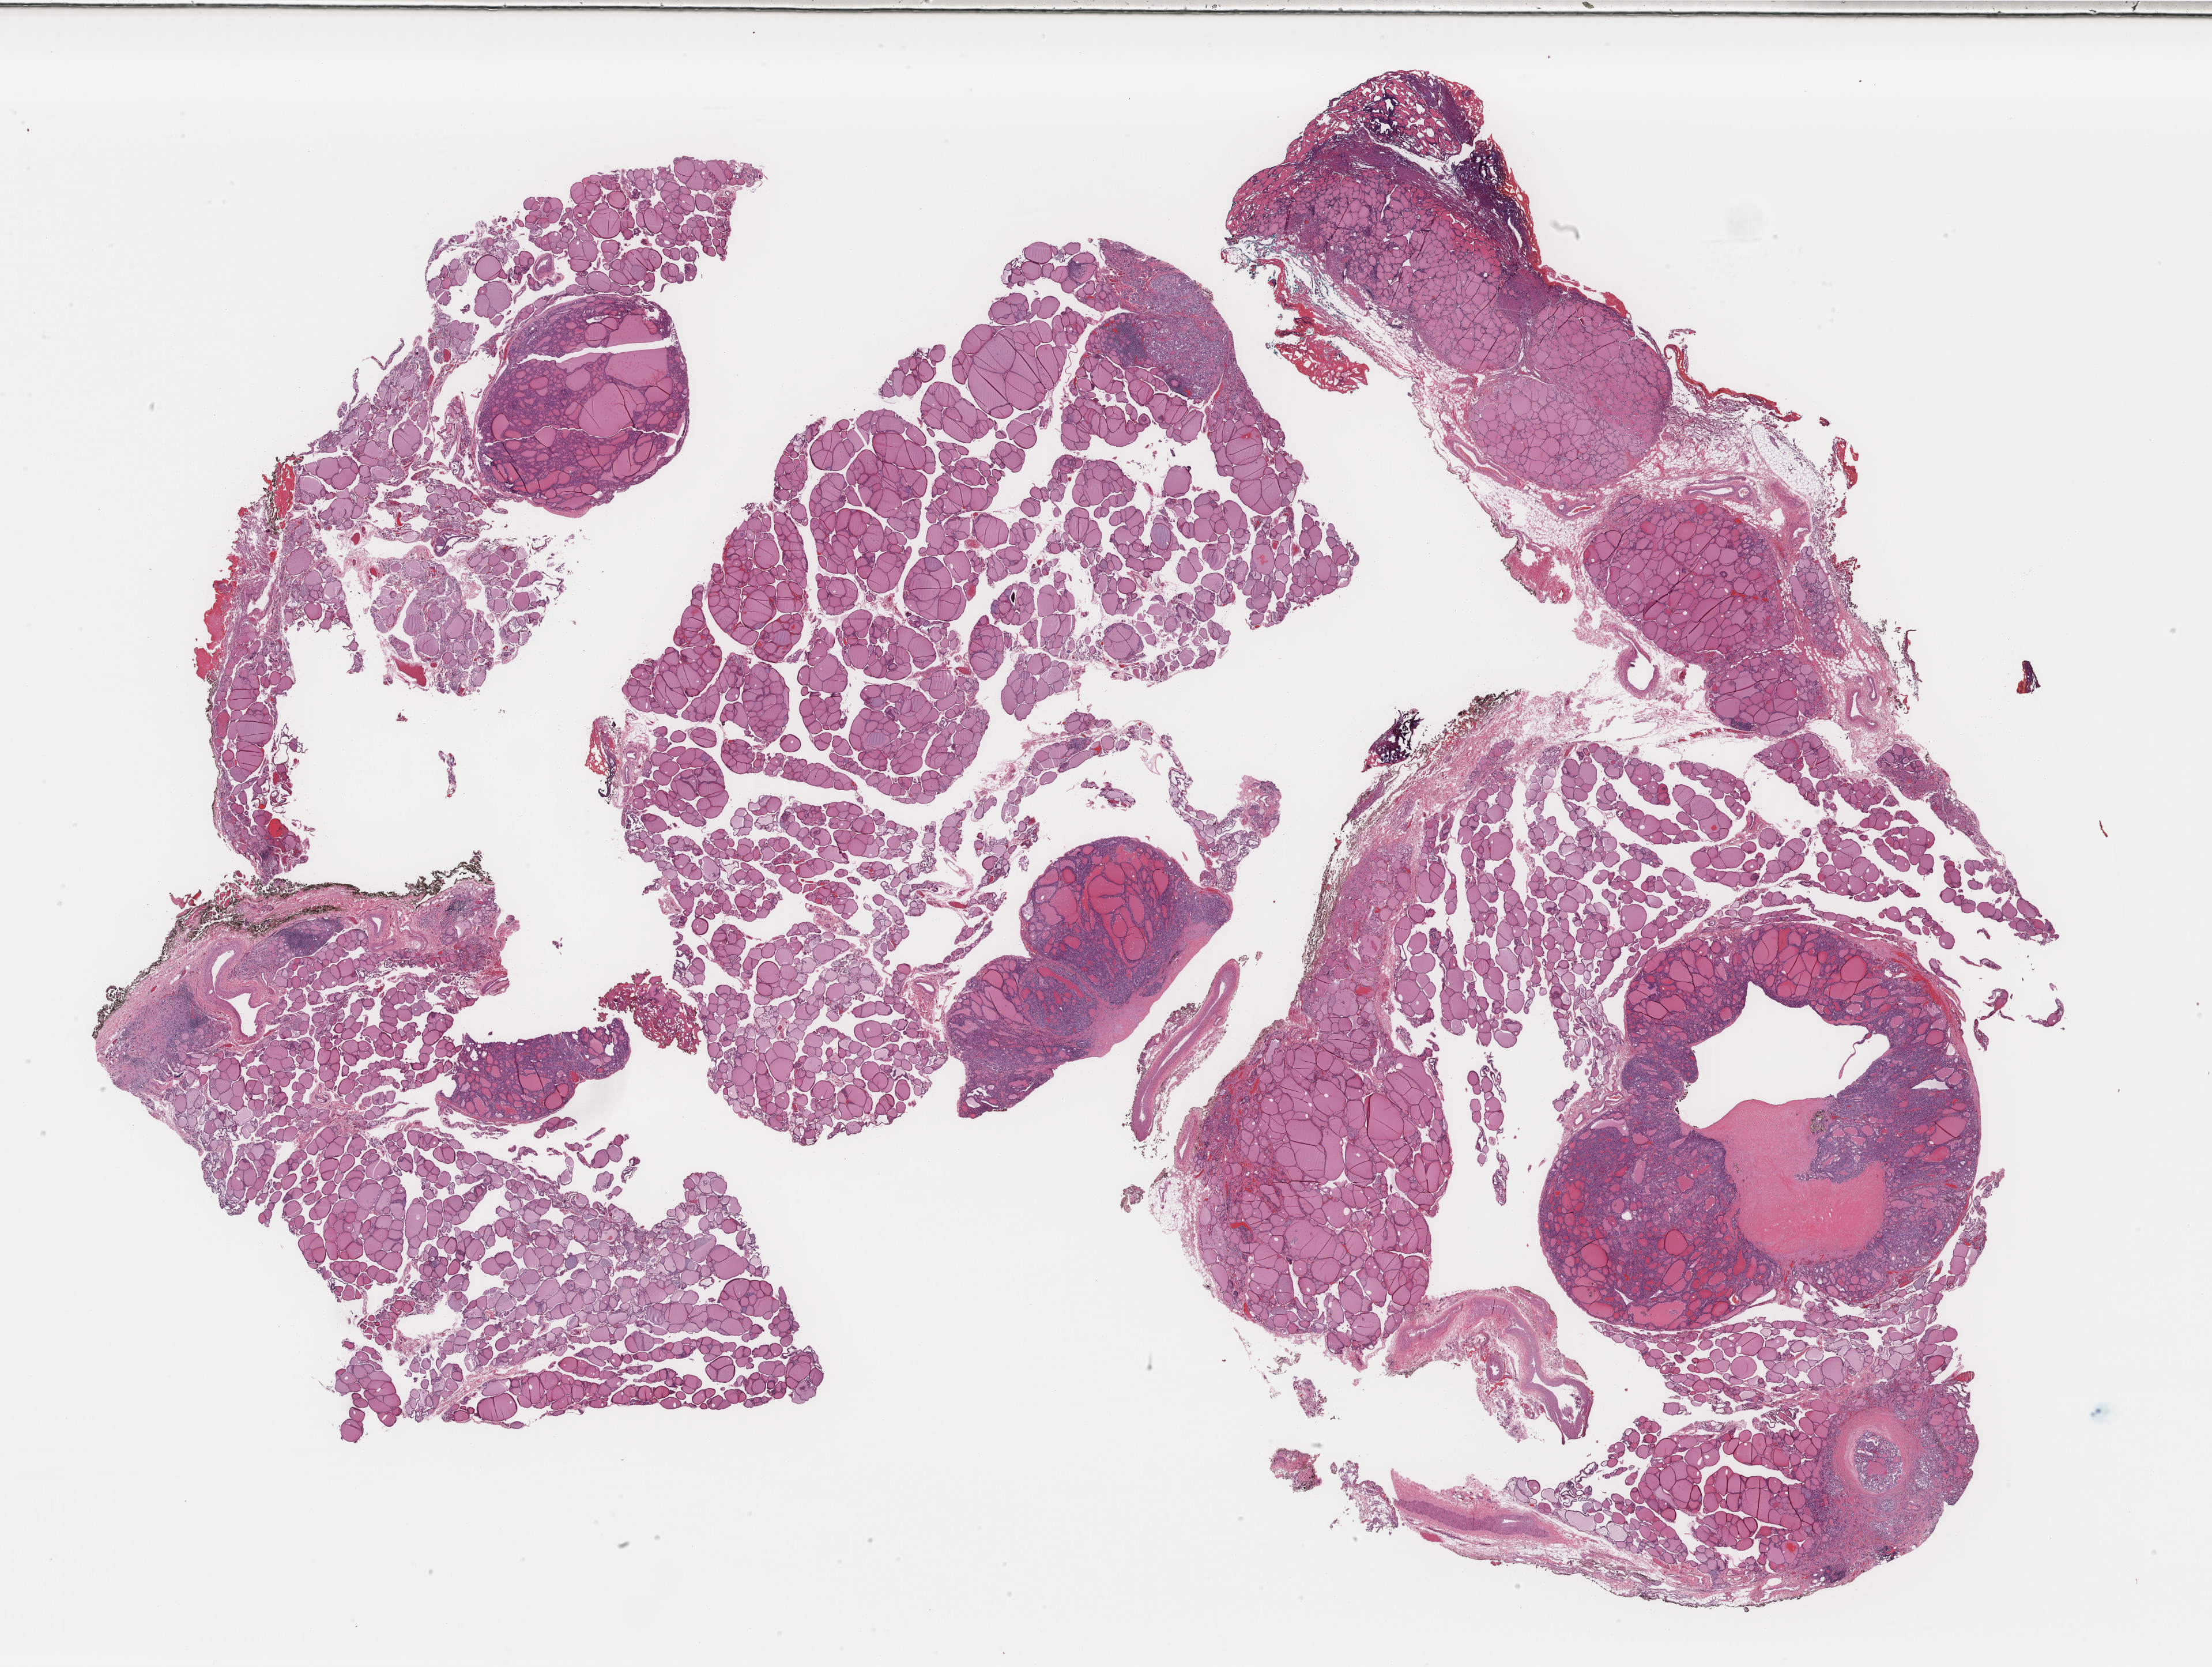
Hematoxylin and eosin (H&E) stained whole-slide image, a low-resolution overview of the entire scanned area, about 30.5 x 23.0 mm. FFPE section. Primary tumour sample from the thyroid. Patient: female, age at initial diagnosis 51 years.
Histologic diagnosis: Papillary adenocarcinoma, NOS (thyroid gland). TNM: T3 N0 M0. AJCC pathologic stage: III.